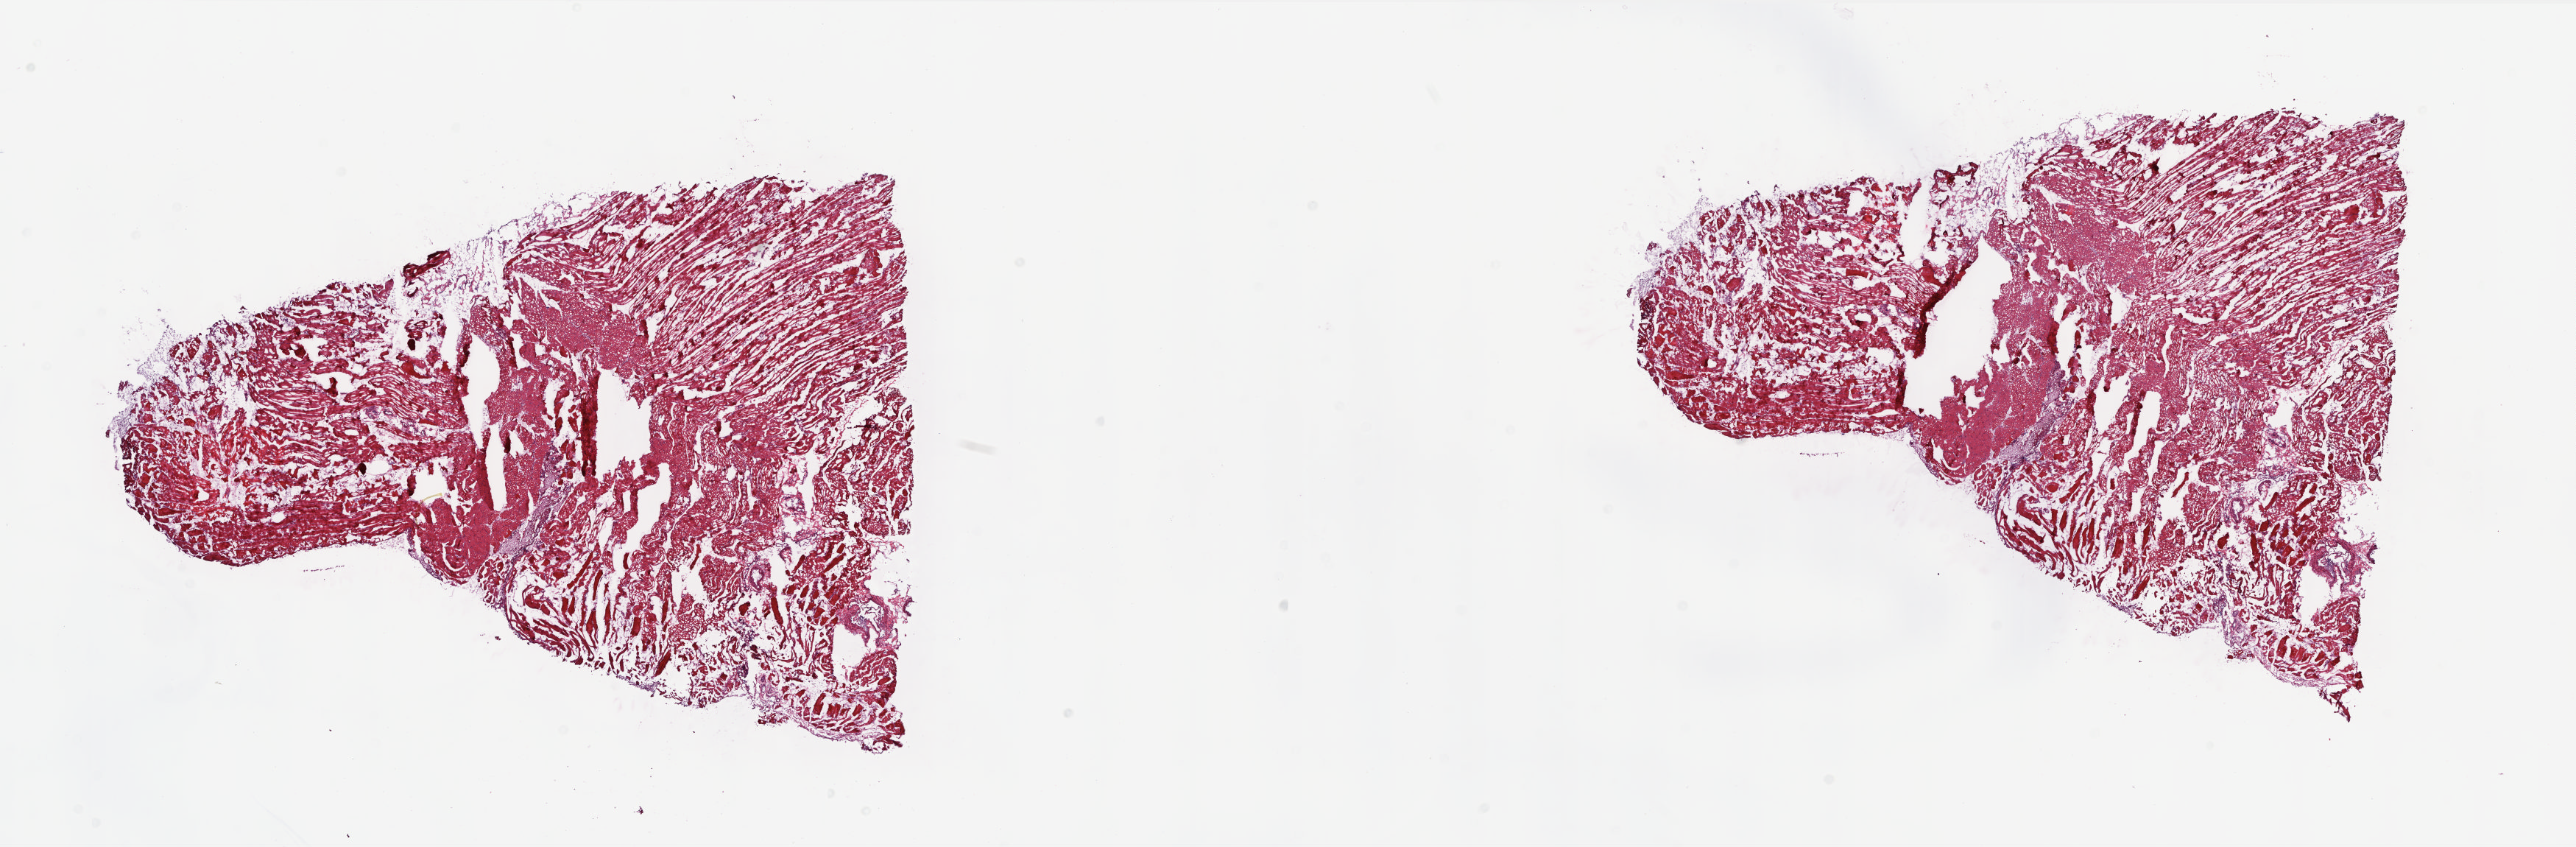
H&E-stained whole-slide image, shown as a low-resolution overview of the whole scanned area (about 27.9 x 9.2 mm, slide scanned at 20x); frozen section from the top of the tissue portion; solid tissue normal (non-tumour tissue) sample from the connective, subcutaneous and other soft tissues. Female patient; age at initial diagnosis 68 years. Composition of this section per pathologist review: tumour cells 0%, tumour nuclei 0%, normal cells 0%, stromal cells 100%, necrosis 0%. Infiltration values recorded for this section: lymphocyte infiltration 1%, monocyte infiltration 1%, neutrophil infiltration 1%.
This section: solid tissue normal sample (biorepository sample class). Patient diagnosis: Undifferentiated sarcoma (connective, subcutaneous and other soft tissues of lower limb and hip).